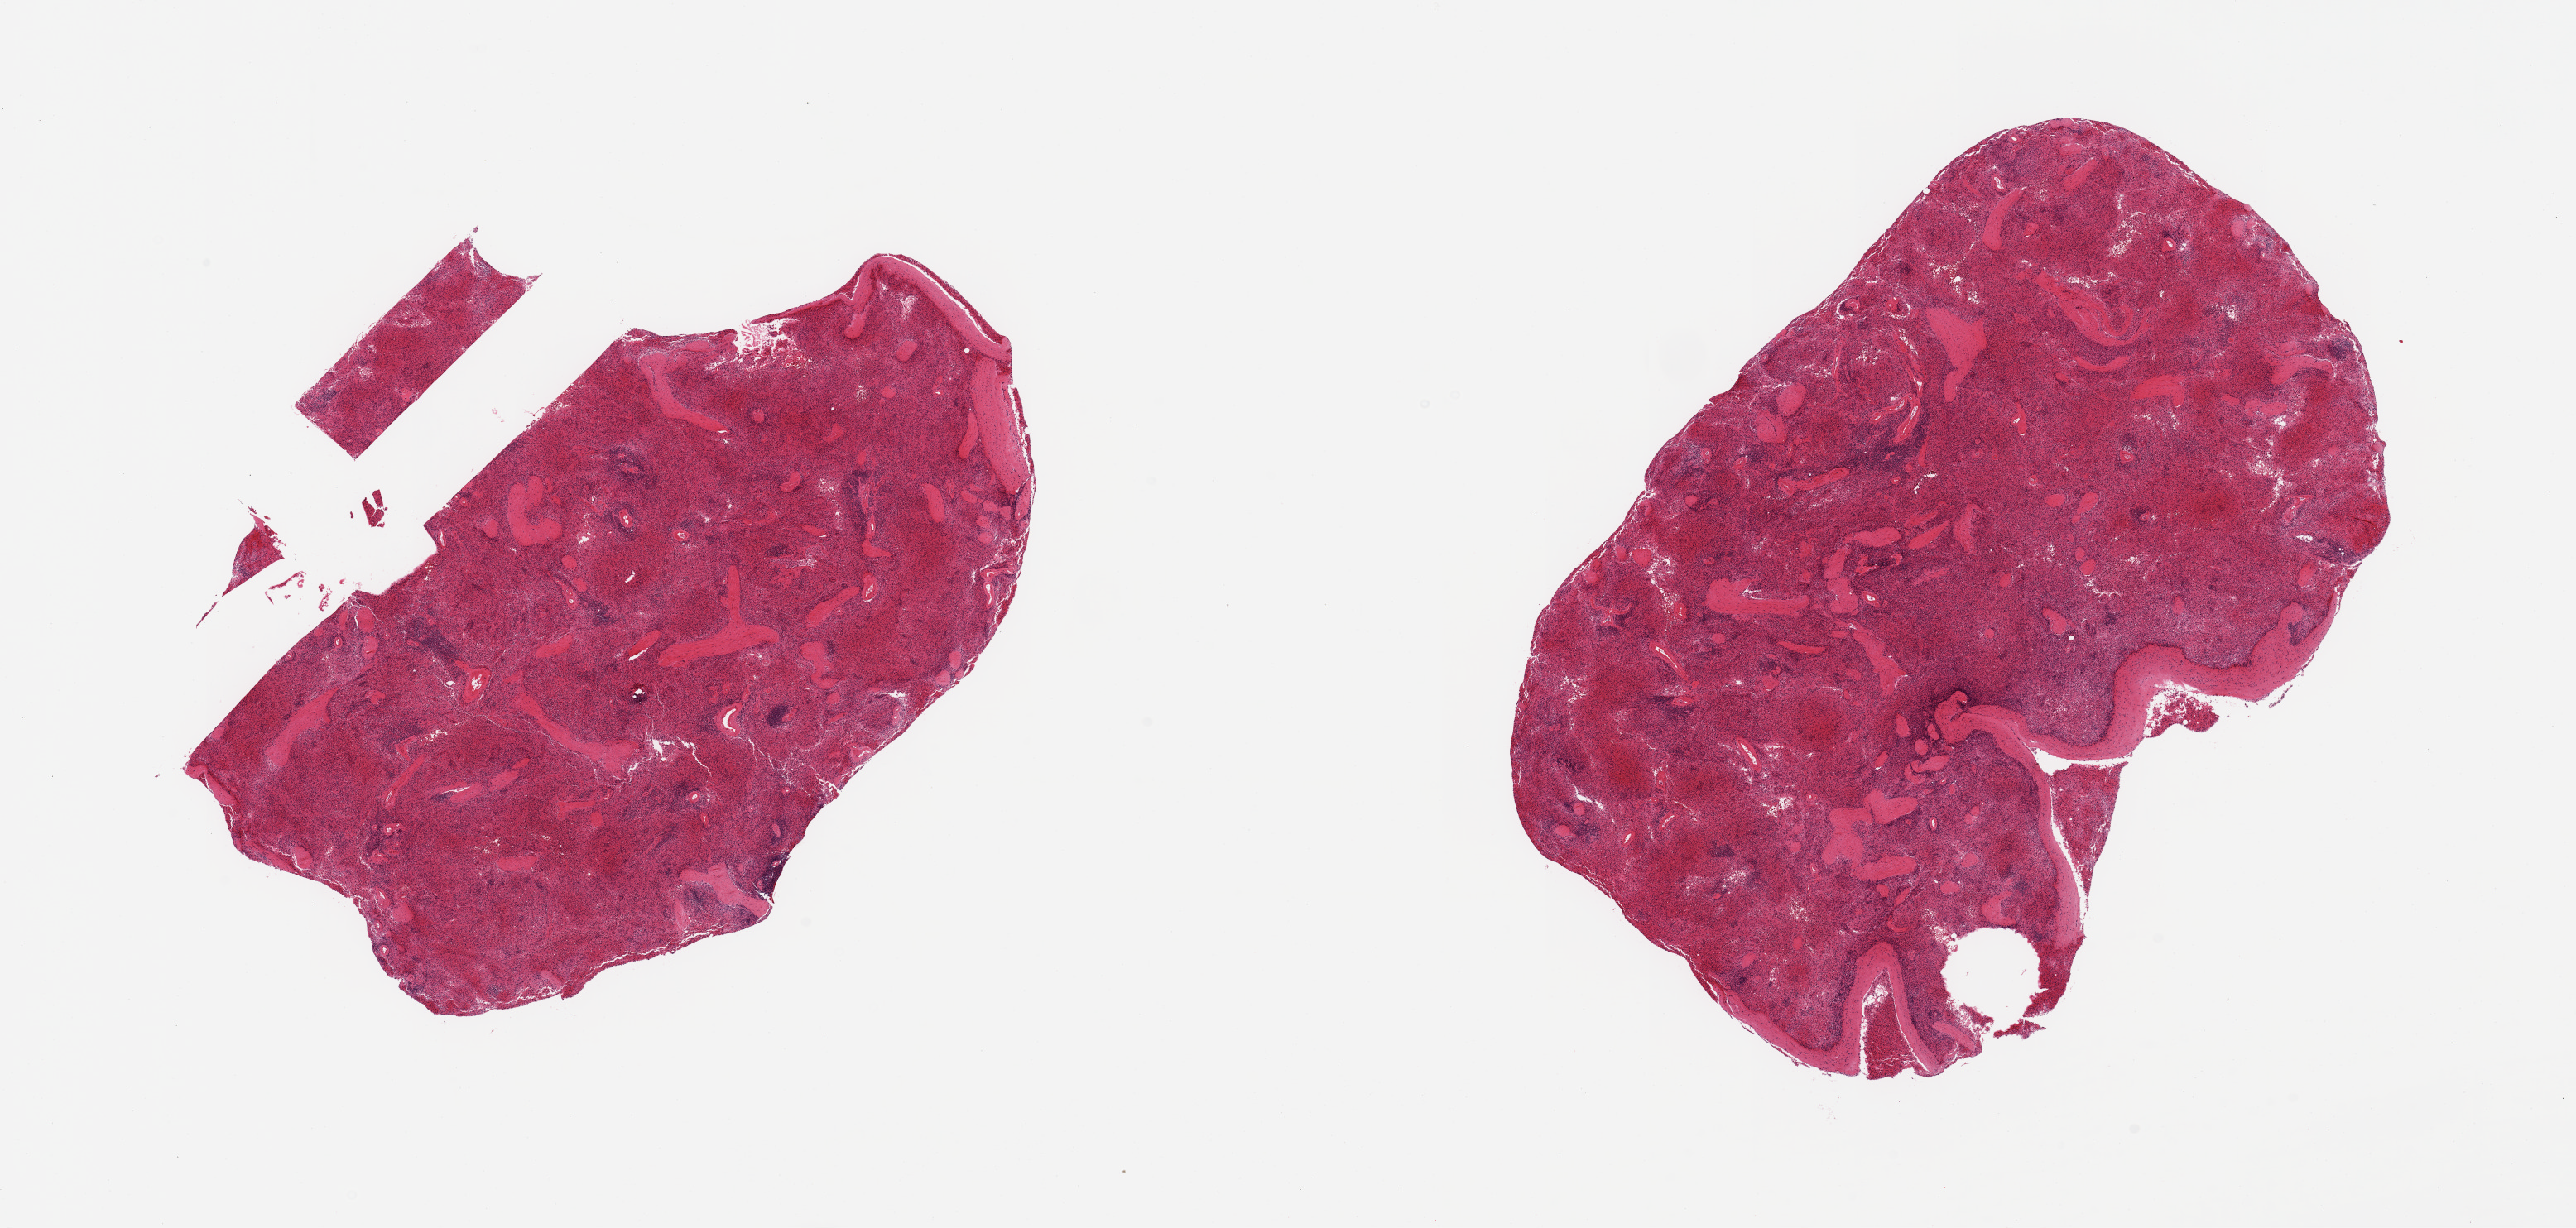
Digitized haematoxylin and eosin-stained section, brightfield — low-resolution overview of the scanned area, about 24.6 x 11.7 mm, PAXgene-fixed paraffin-embedded (PFPE) section, section of spleen (target tissue), tissue donor sample. Donor: male.
* review note (as recorded): 2 pieces; moderate congestion